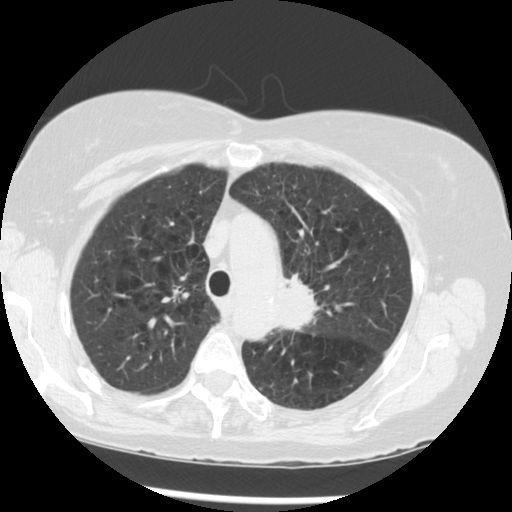
Low-dose screening chest CT, one axial slice. Position 212 of 283 along the scan axis. Reconstruction kernel STANDARD. 120 kVp. Lung window (W 1500 / L -600 HU). 2.5 mm slice thickness. 512 × 512 image matrix, field of view 330 × 330 mm.
Structures marked on this image (outlined manually by an expert reader):
- lesion 1 (tumor, upper lobe of left lung): bounding box [x1, y1, x2, y2] px = [278, 275, 317, 330]